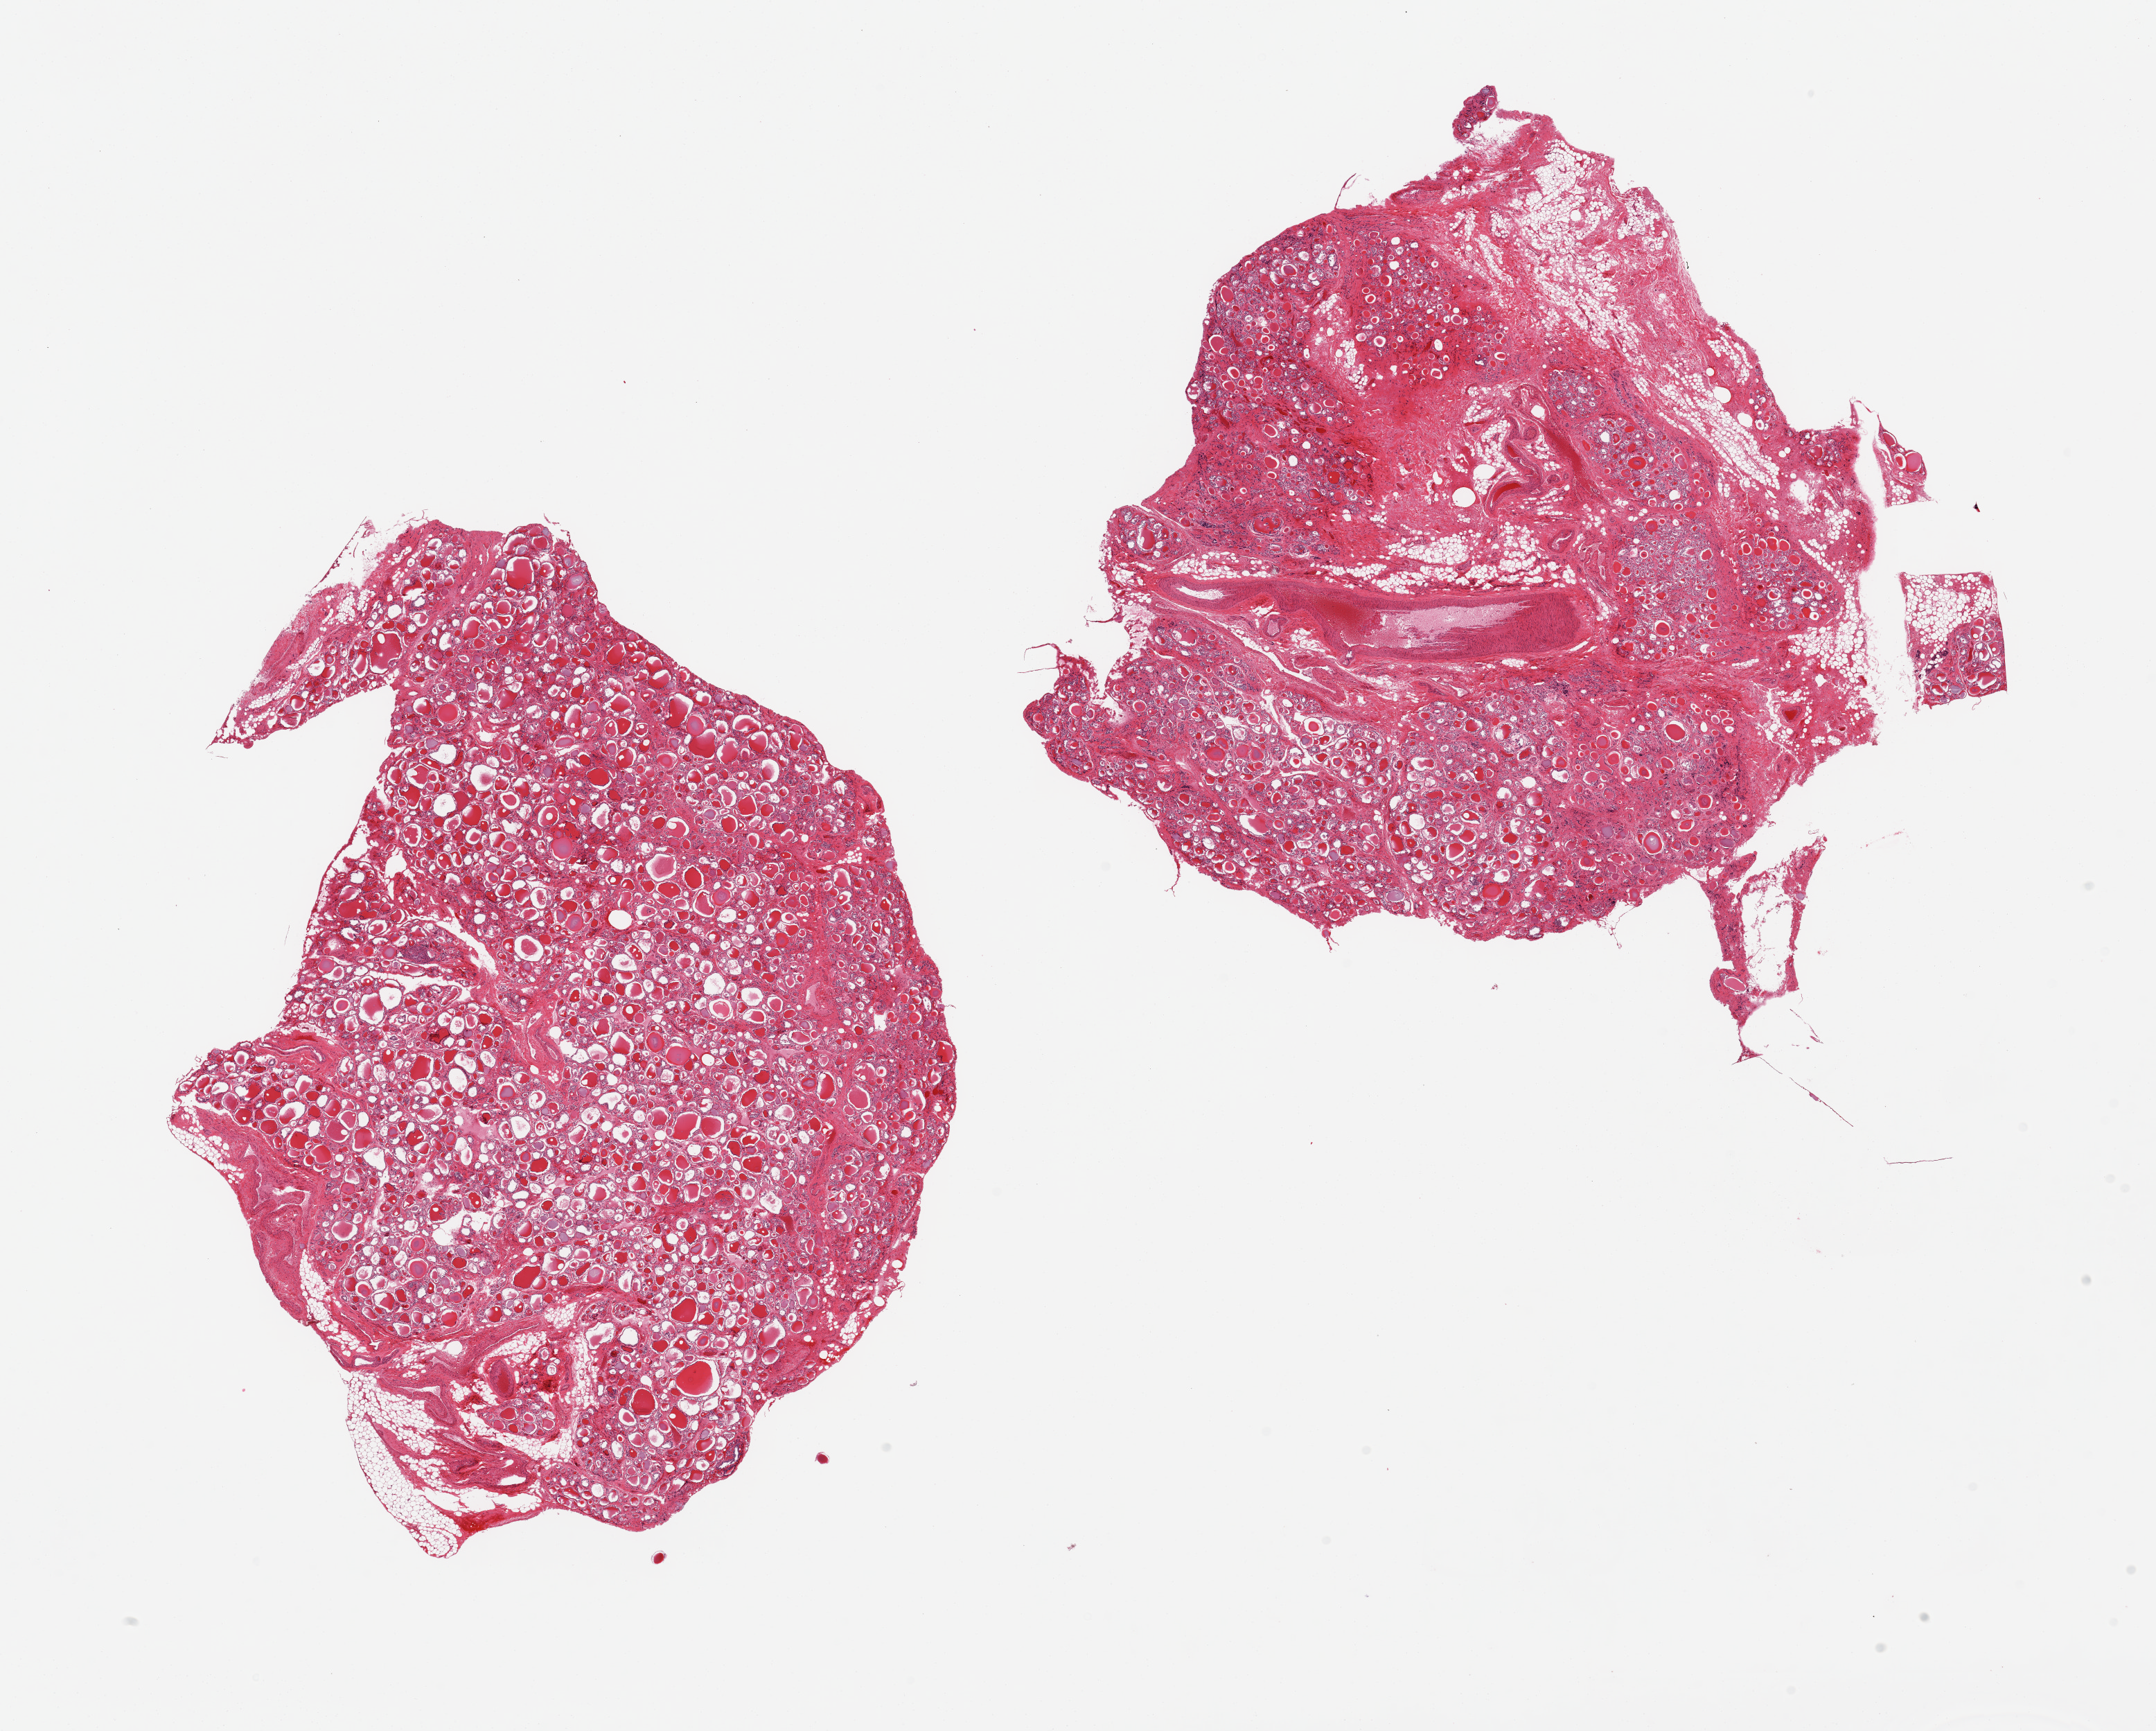
Whole-slide image, haematoxylin and eosin stain — low-resolution overview of the scanned area, about 24.6 x 19.8 mm; PAXgene-fixed, paraffin-embedded tissue; target tissue: thyroid; tissue donor sample. Donor sex: male.
Reviewer comment on this tissue sample: 2 pieces; interstitial fibrosis with associated atrophy of follicles, both include region of fat and large vessels (10% and 30%).